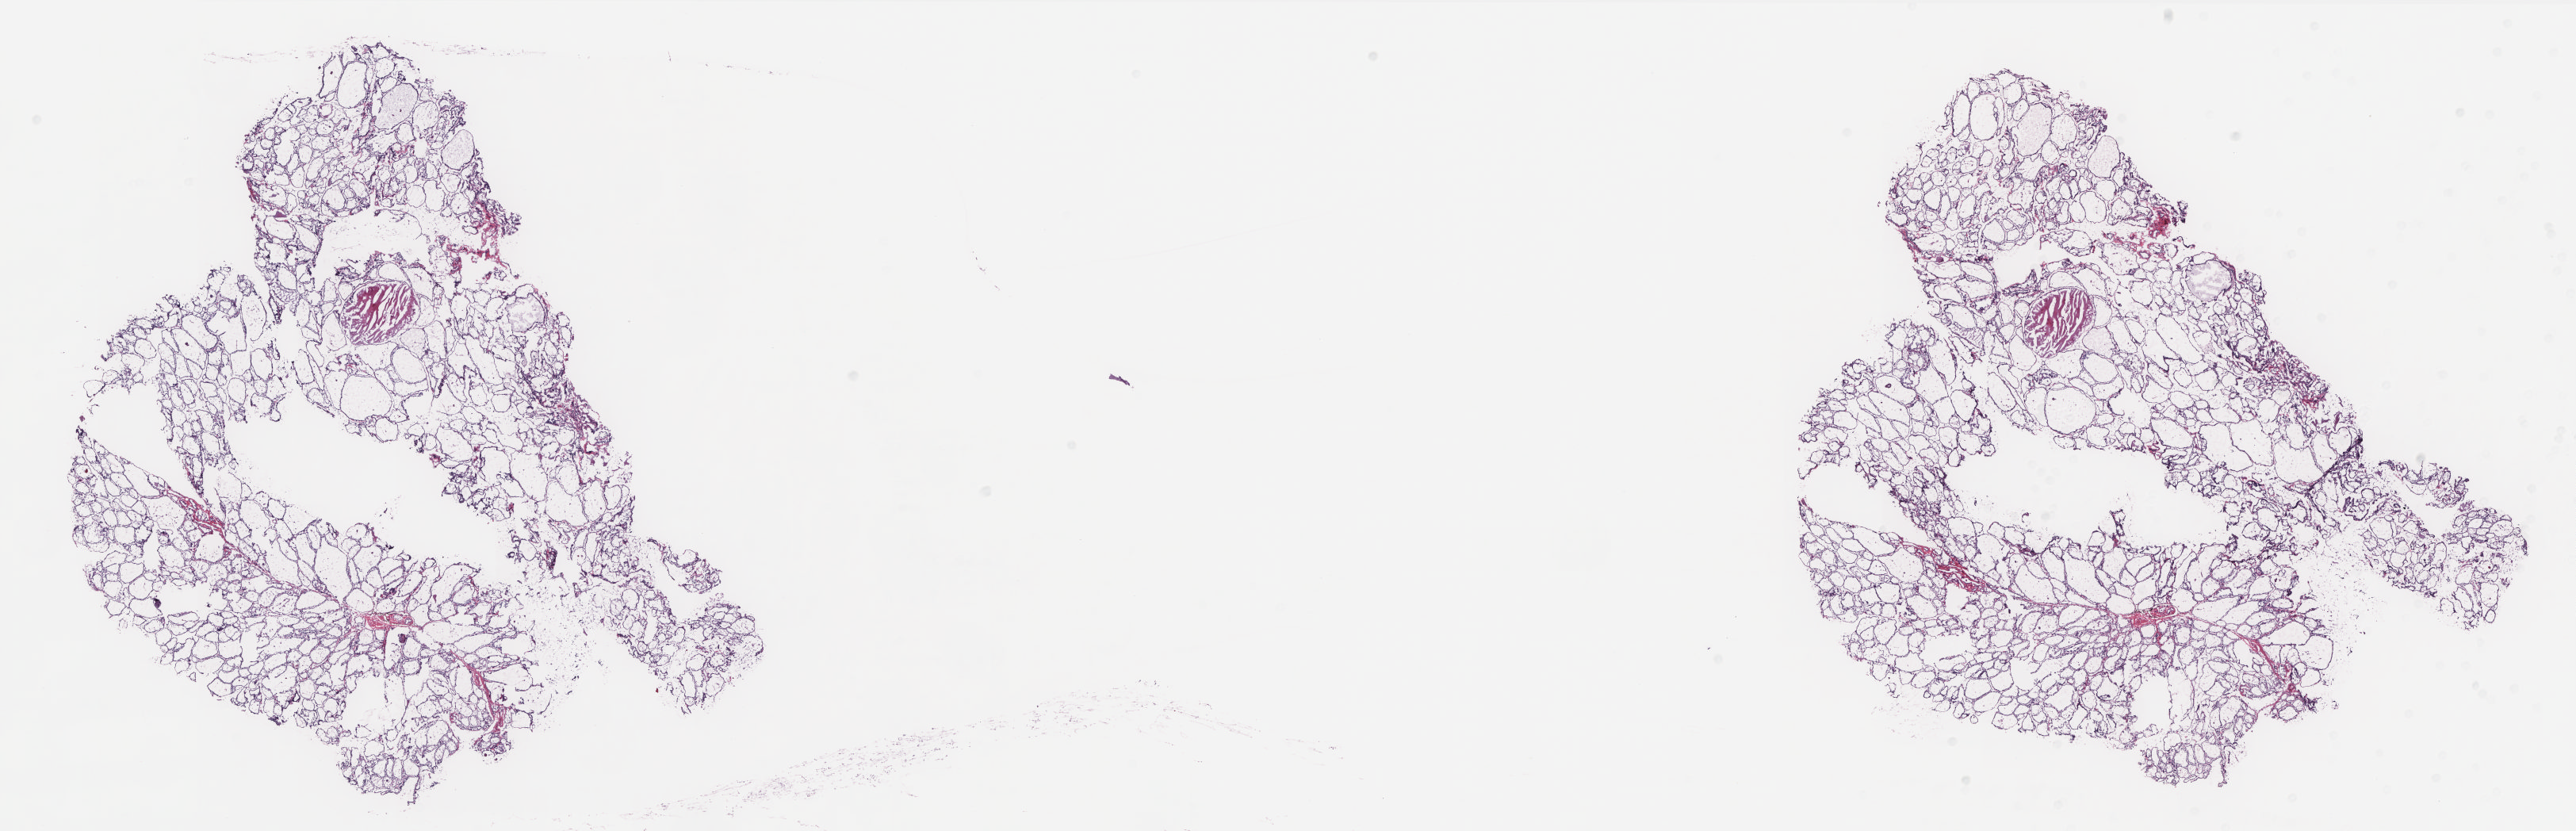
Whole-slide histology image, H&E — shown as a low-resolution overview of the whole scanned area (about 25.9 x 8.4 mm, slide scanned at 20x); frozen section from the top of the tissue portion; thyroid, solid tissue normal (non-tumour tissue) sample. Female, age 46 years at initial diagnosis. Composition of this section per pathologist review: tumour cells 0%, tumour nuclei 0%, normal cells 100%, stromal cells 0%, necrosis 0%. Inflammatory infiltration, as recorded: lymphocyte infiltration 2%, monocyte infiltration 2%, neutrophil infiltration 0%.
This section: solid tissue normal (non-tumour) sample from the same patient. Patient diagnosis: Papillary carcinoma, follicular variant.